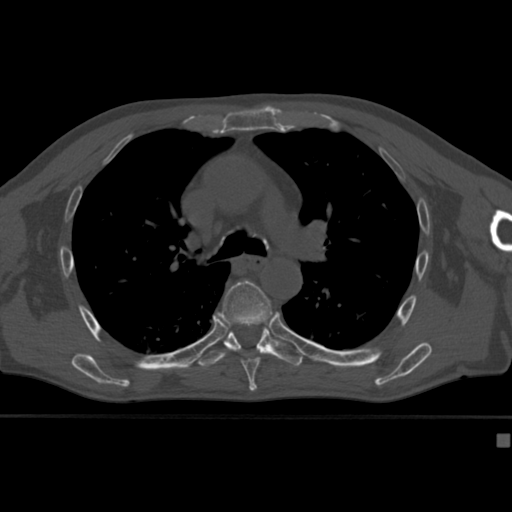
CT including the spine, one axial slice. Slice 288 of 430 in the series (ordered by position). 120 kVp. Bone window (W 1800 / L 400 HU). 512 × 512 image matrix. Patient: male, 64 years. Case-level facts recorded for this patient, not image findings: primary cancer: uterus.
Structures marked on this image (semi-automatic segmentation, software-assisted and operator-edited):
- T6 vertebra: bounding box <201,280,272,382> (left, top, right, bottom; pixels)
- T7 vertebra: <198,327,304,369>